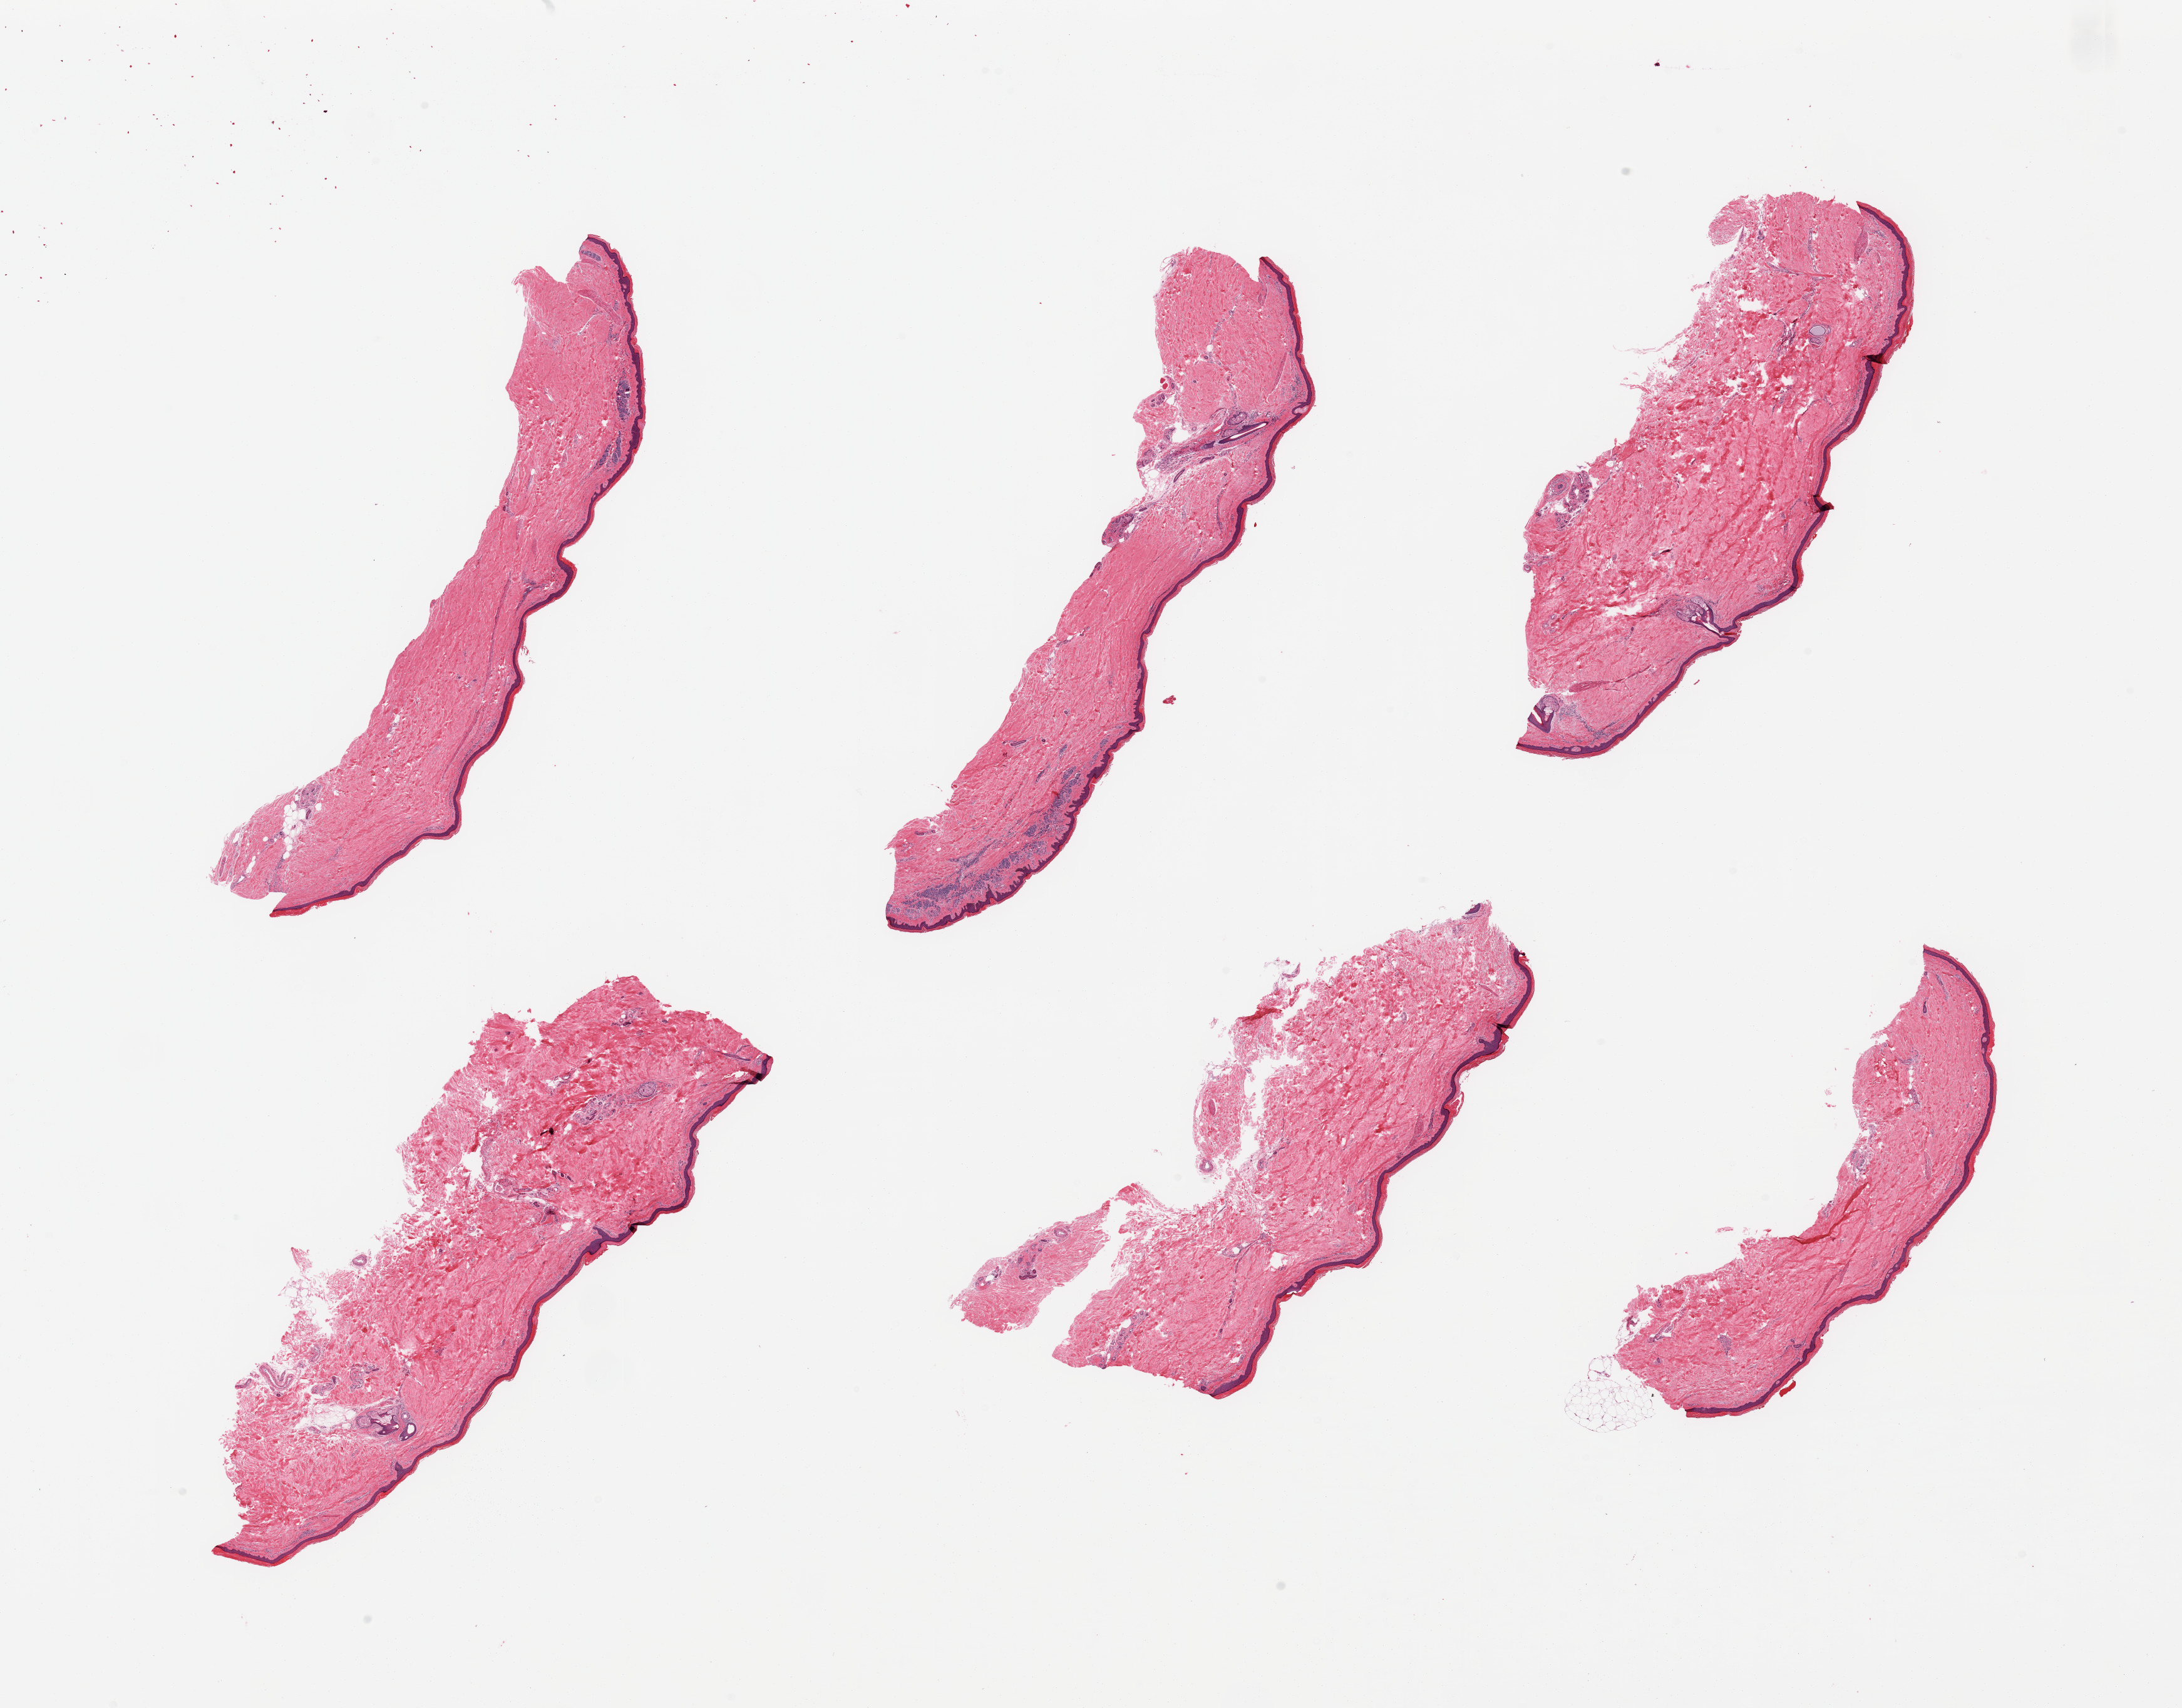
Whole-slide image, H&E stain, brightfield, low-resolution overview of the scanned area, about 27.6 x 21.6 mm (slide scanned at 20x); PAXgene-fixed, paraffin-embedded tissue; sampled site (target tissue): skin of lower leg; donor tissue sample.
- pathologist's review note for this sample: 6 pieces; intradermal nevus in 2 of 6 pieces; well trimmed; 1% dermal fat